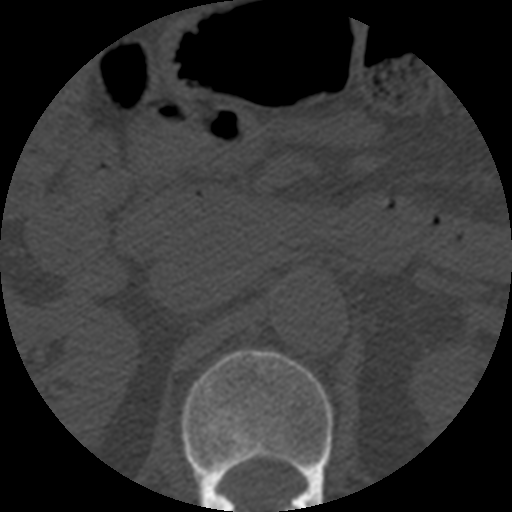
CT including the spine, one axial slice; position 192 of 508 along the scan axis; 120 kVp; bone window (W 1800 / L 400 HU); 1.25 mm slice thickness; 512 × 512 image matrix, field of view 160 × 160 mm. Patient age 57 years. From the clinical record (not read from this slice): primary cancer: prostate.
Outlined on this slice (semi-automatically segmented with operator editing):
- L1 vertebra: bounding box <181,350,333,512> (left, top, right, bottom; pixels)